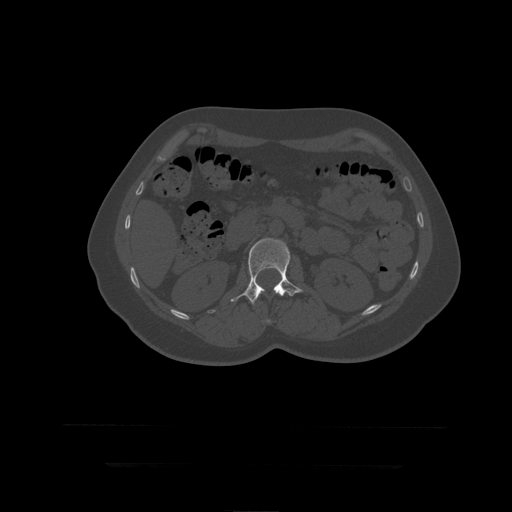
CT including the spine, one axial slice; slice 152 of 399 in the series (ordered by position); reconstruction kernel STANDARD; 120 kVp; bone window (W 1800 / L 400 HU); 1.25 mm slice thickness; 512 × 512 image matrix. Patient age 41 years. From the clinical record (not read from this slice): primary cancer: breast.
Structures marked on this image (semi-automatically segmented with operator editing):
- L1 vertebra: box from (x=267, y=320) to (x=270, y=323) px
- L2 vertebra: (x=231, y=238)–(x=304, y=305)